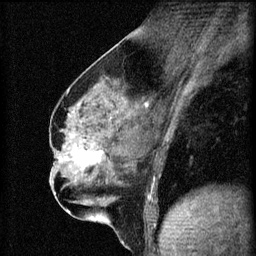
Breast MRI (dynamic contrast-enhanced), one sagittal slice. 3 images stored at this slice position (order not interpretable as contrast timing). 1.5 T. TE 4.2 ms, TR 8.2 ms. 2 mm slice thickness. 256 × 256 image matrix, field of view 180 × 180 mm. Female patient, age 56 years.
Structures marked on this image (semi-automatic segmentation, software-assisted and operator-edited):
- analysis volume of interest (the breast-tissue region the enhancement analysis was run in; not a lesion): bounding box [x1, y1, x2, y2] px = [62, 136, 111, 179]
- tumour enhancement mask (voxels above the 70 % enhancement threshold inside the analysis volume of interest): [62, 142, 103, 165]